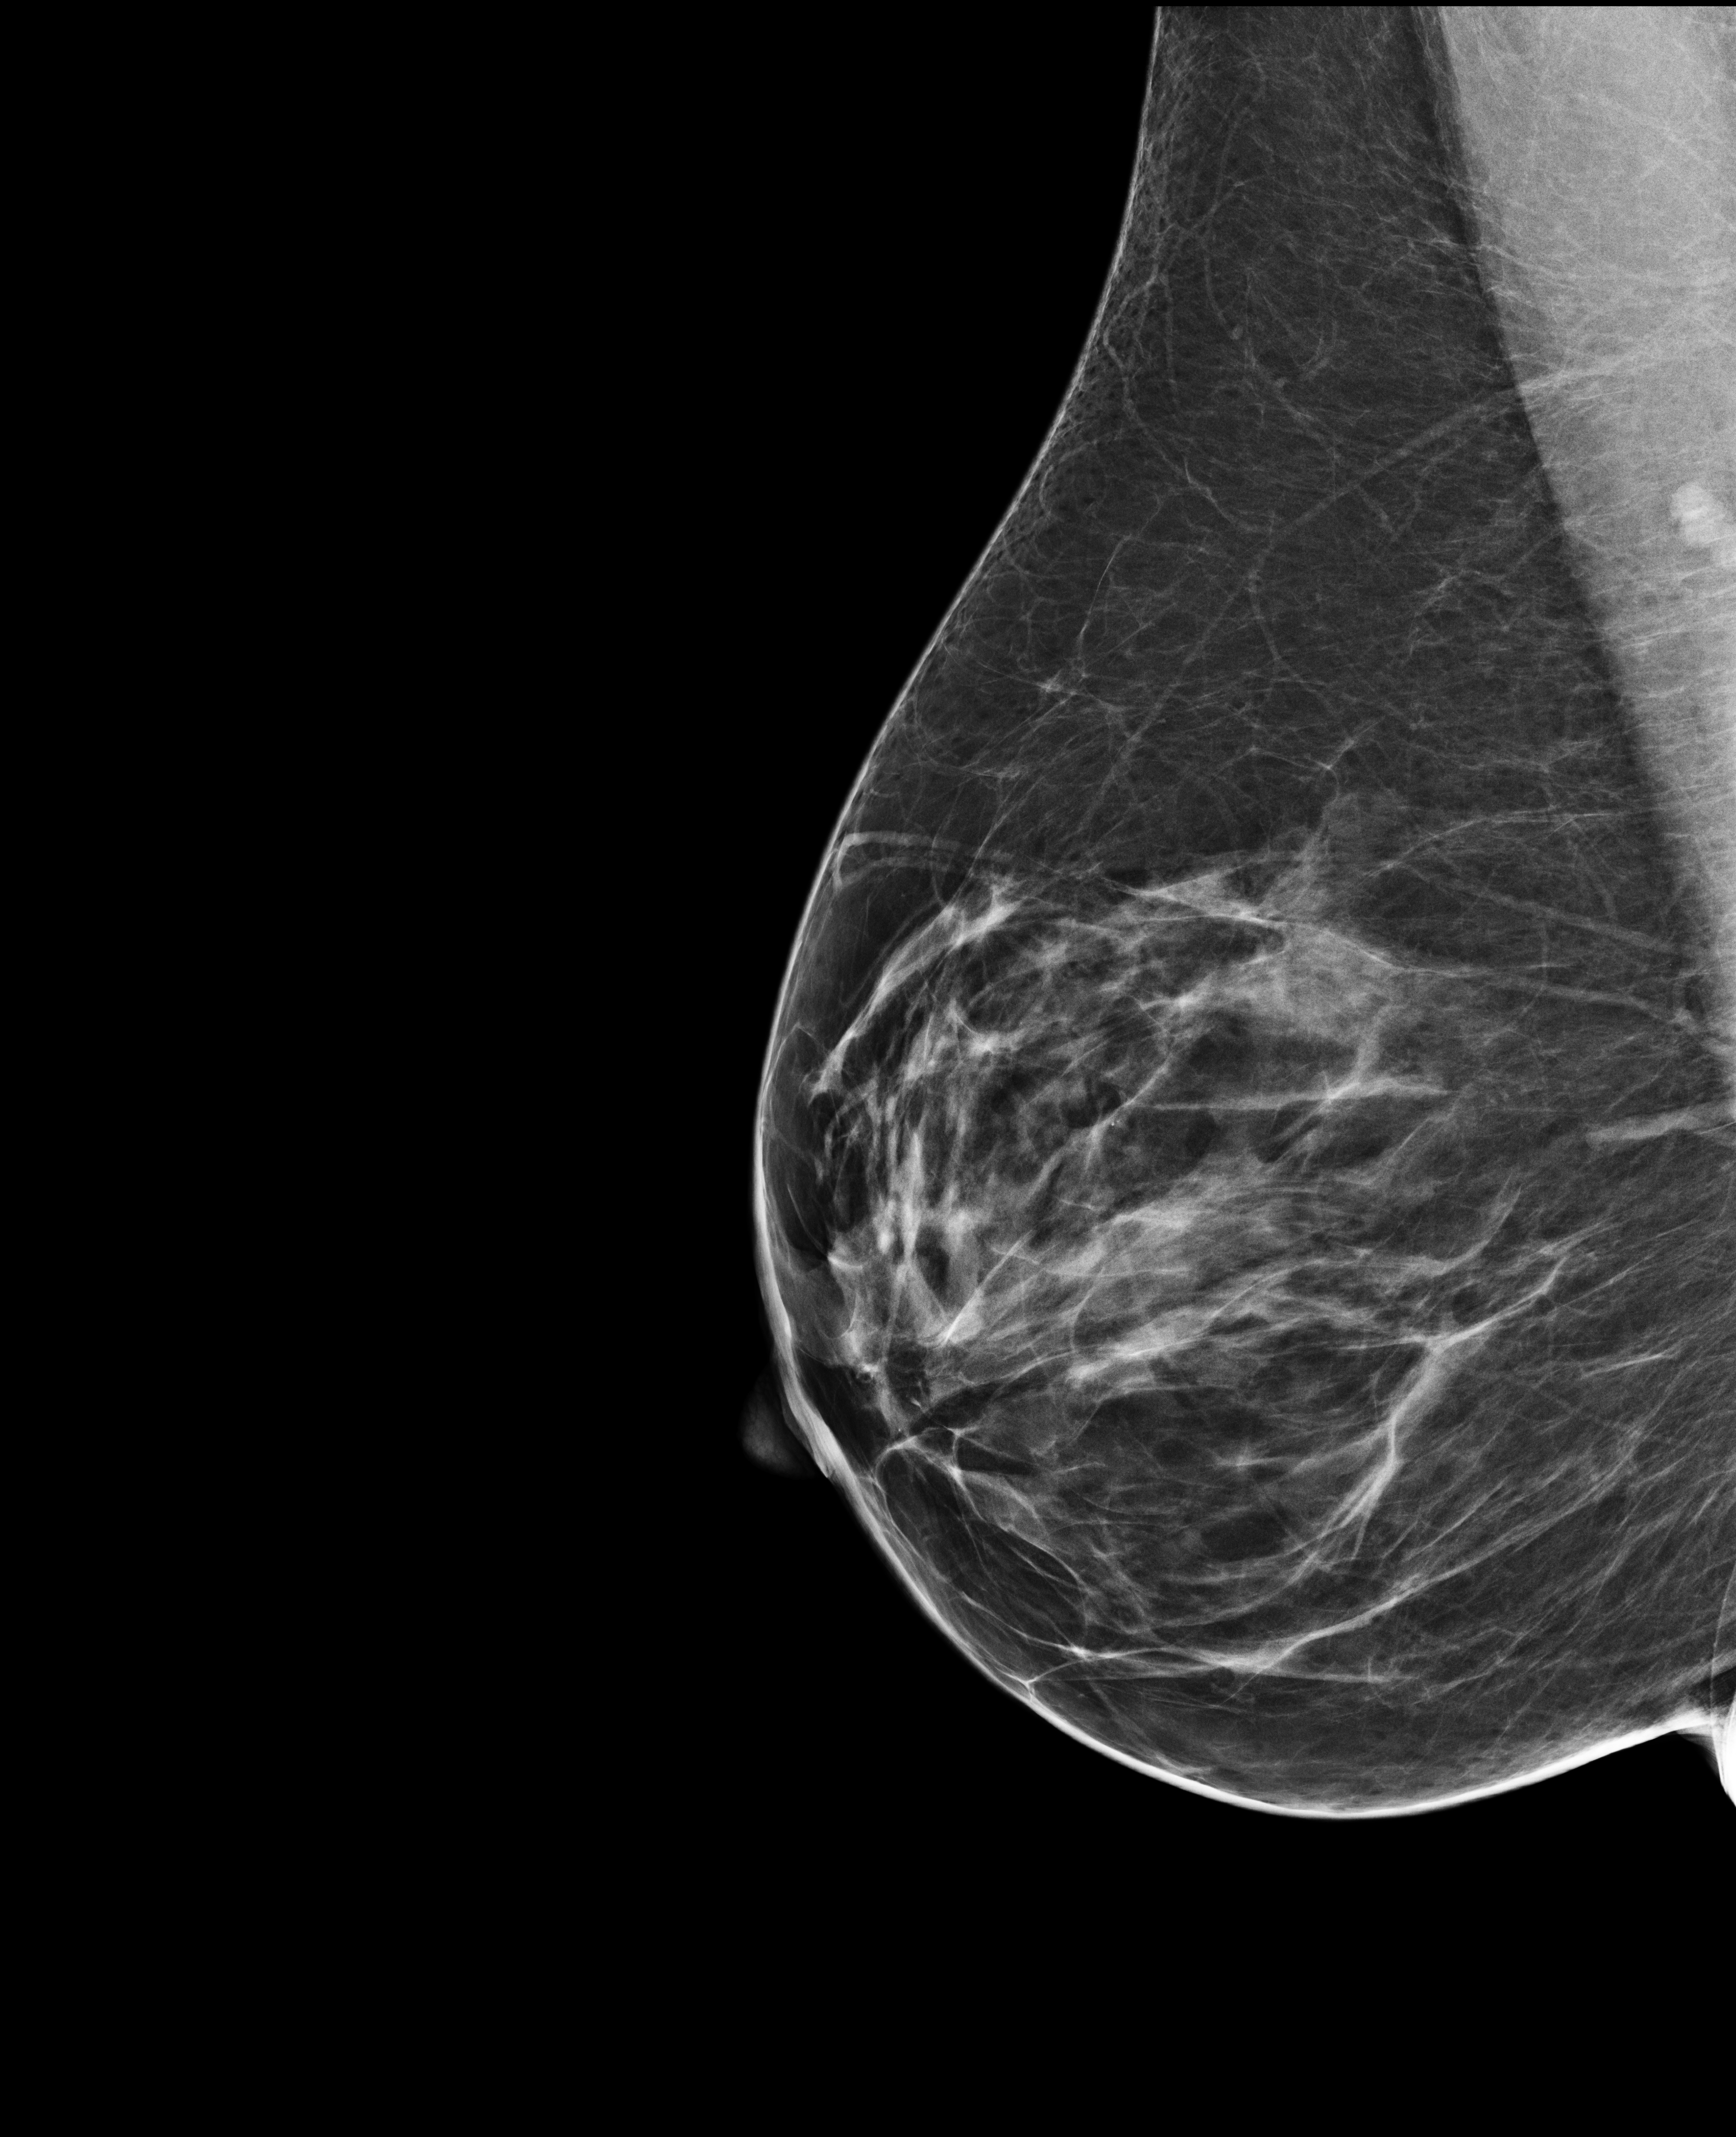
Annual screening mammography examination, compressed breast thickness 78 mm. Female patient, age 58 years.
Image type: full-field digital mammogram. Breast: right. Projection: medio-lateral oblique projection.